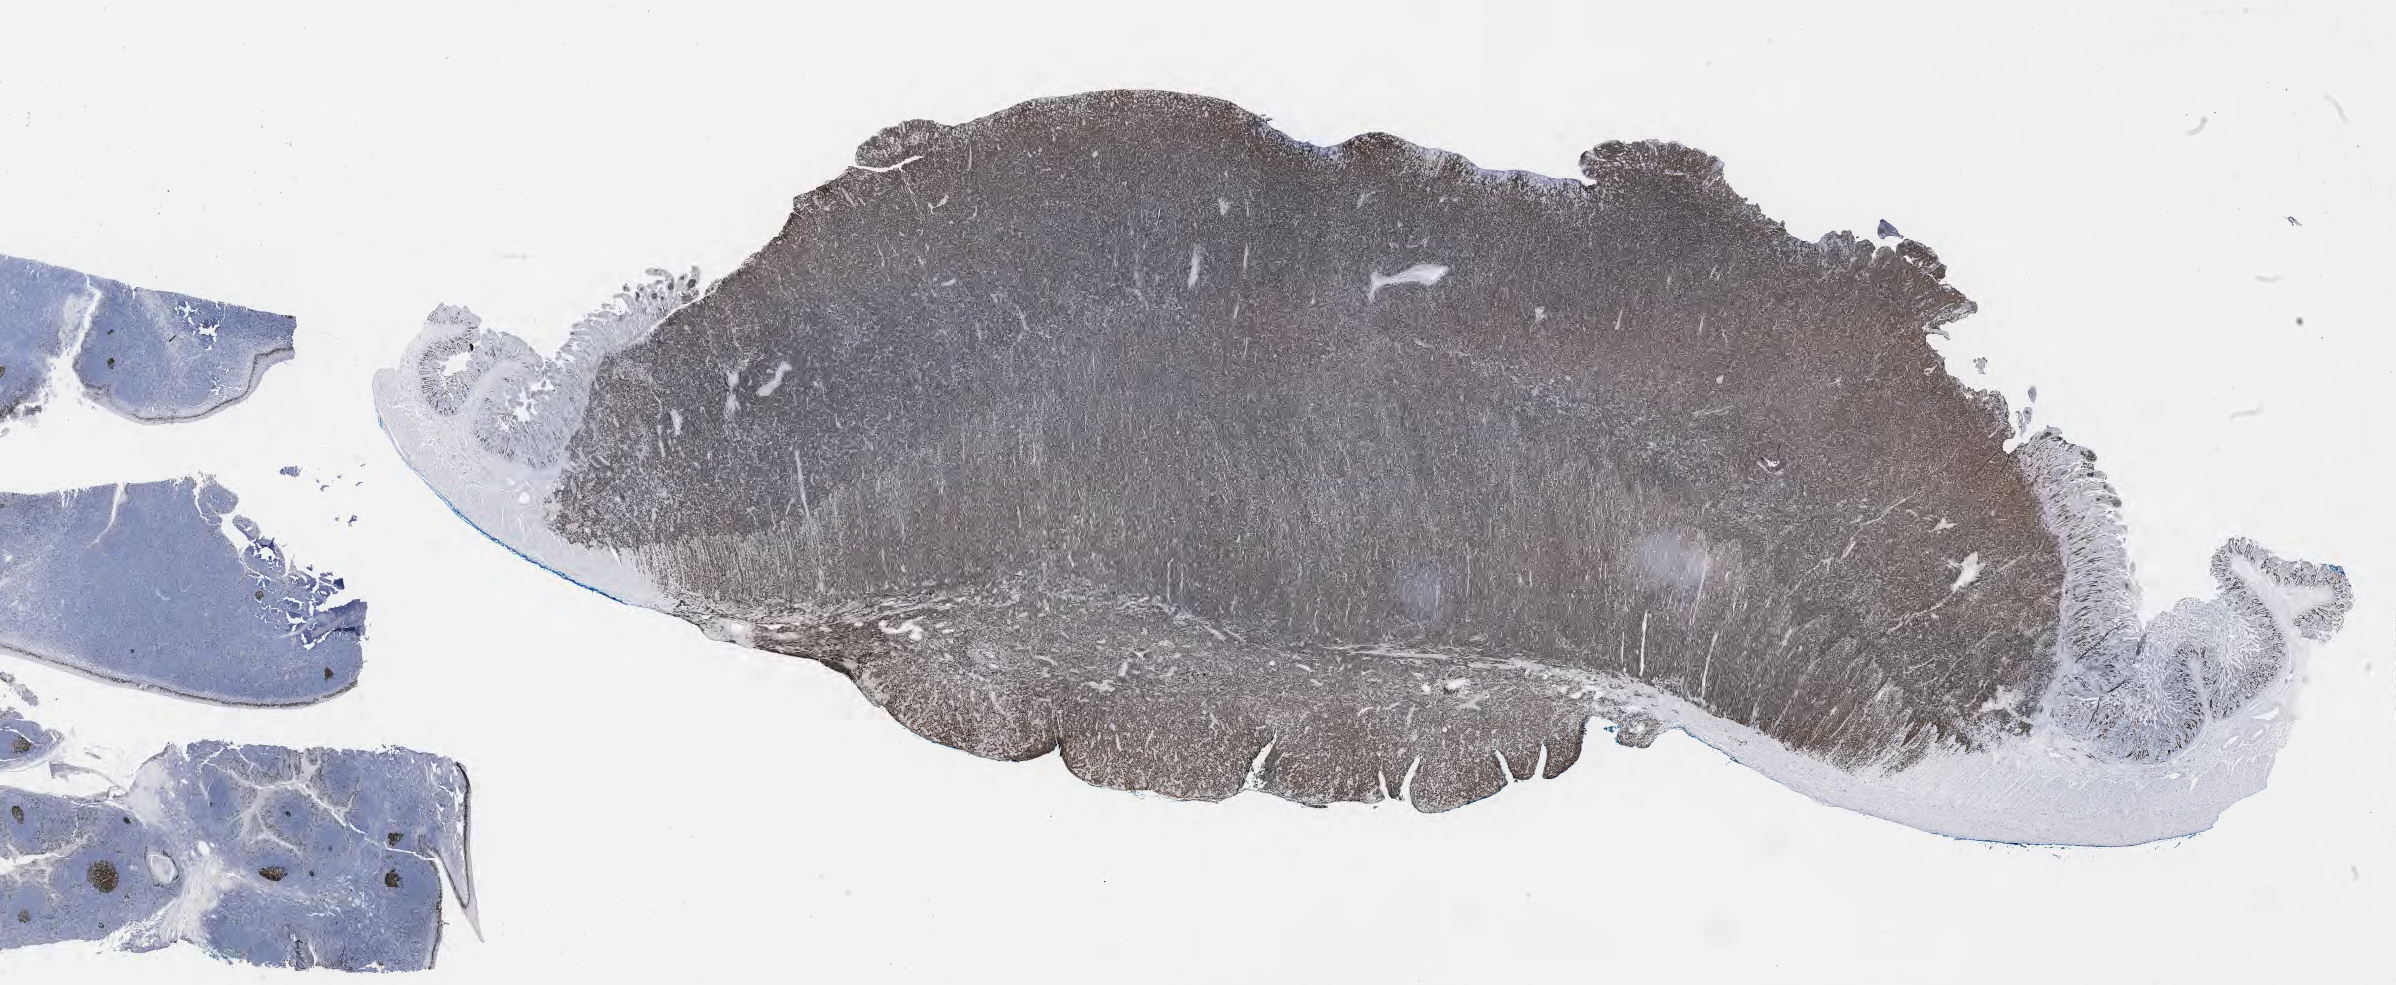
Immunohistochemistry (IHC) whole-slide image stained for Ki-67, a low-resolution overview of the entire scanned area, about 38.7 x 15.9 mm. Tumor tissue. Site: small intestine. Patient: male, age at initial diagnosis 6 years.
Histologic diagnosis: Burkitt lymphoma, NOS.